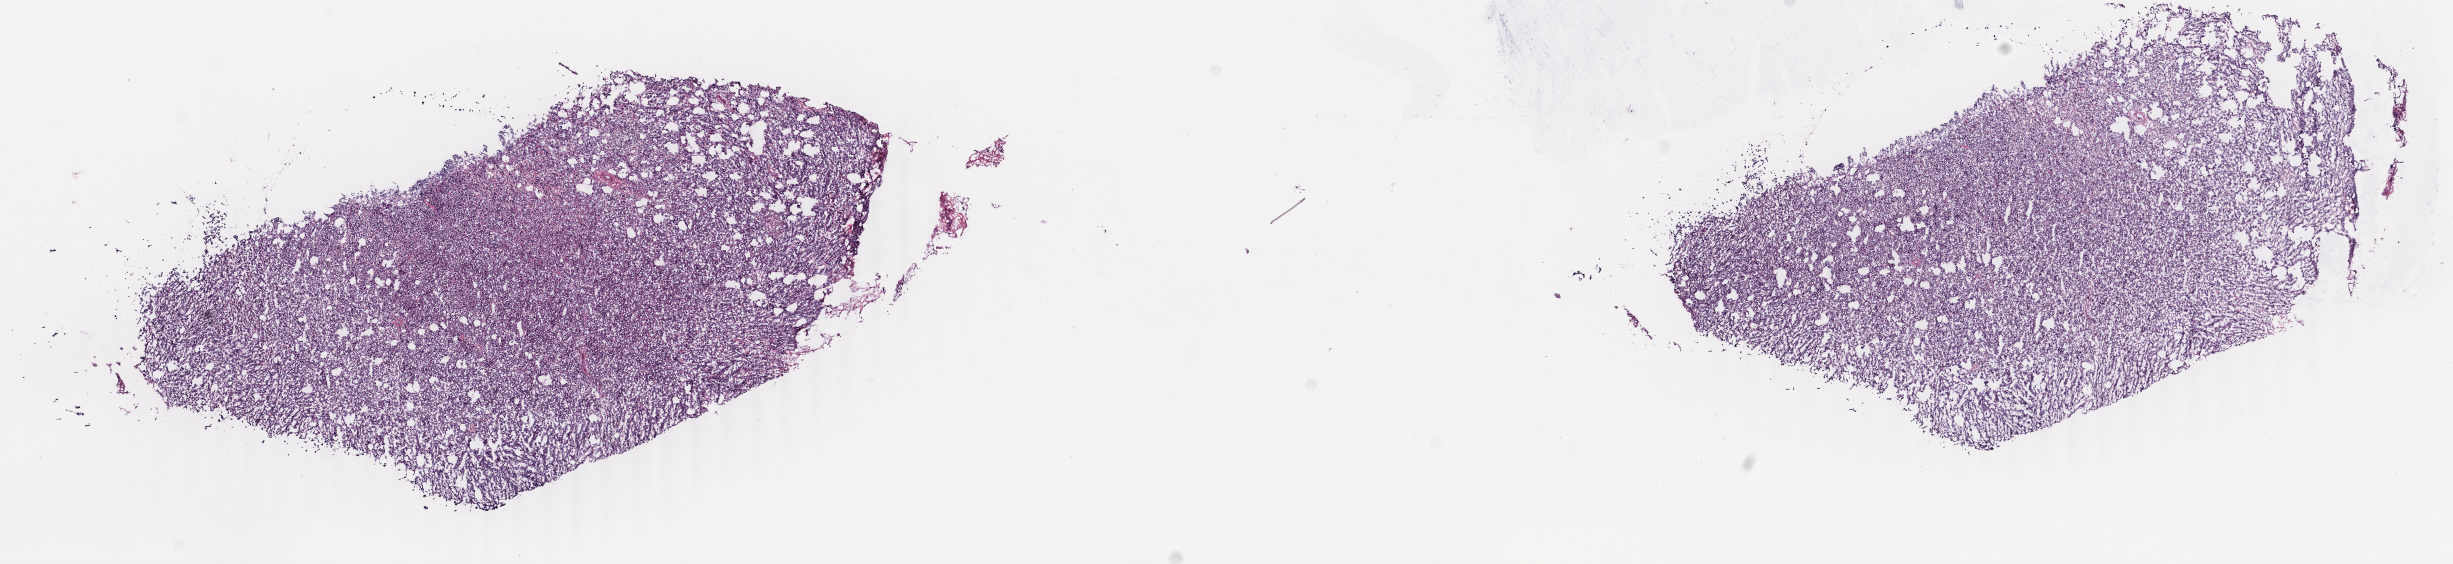
Whole-slide histology image, H&E-stained, low-resolution overview of the scanned area, about 19.5 x 4.5 mm (from a 40x scan), frozen section from the top of the tissue portion, breast, primary tumour sample. Patient: female, age at initial diagnosis 65 years. Slide review estimates, as recorded: tumour cells 90%, tumour nuclei 90%, normal cells 0%, stromal cells 8%, necrosis 2%. Inflammatory infiltration, as recorded: lymphocyte infiltration 1%, monocyte infiltration 1%, neutrophil infiltration 1%.
AJCC pathologic stage: IIA (5th edition). Lymph nodes positive (case pathology): 0 of 4 examined. Pathologic diagnosis: Lobular carcinoma, NOS. TNM: T2 N0 M0.